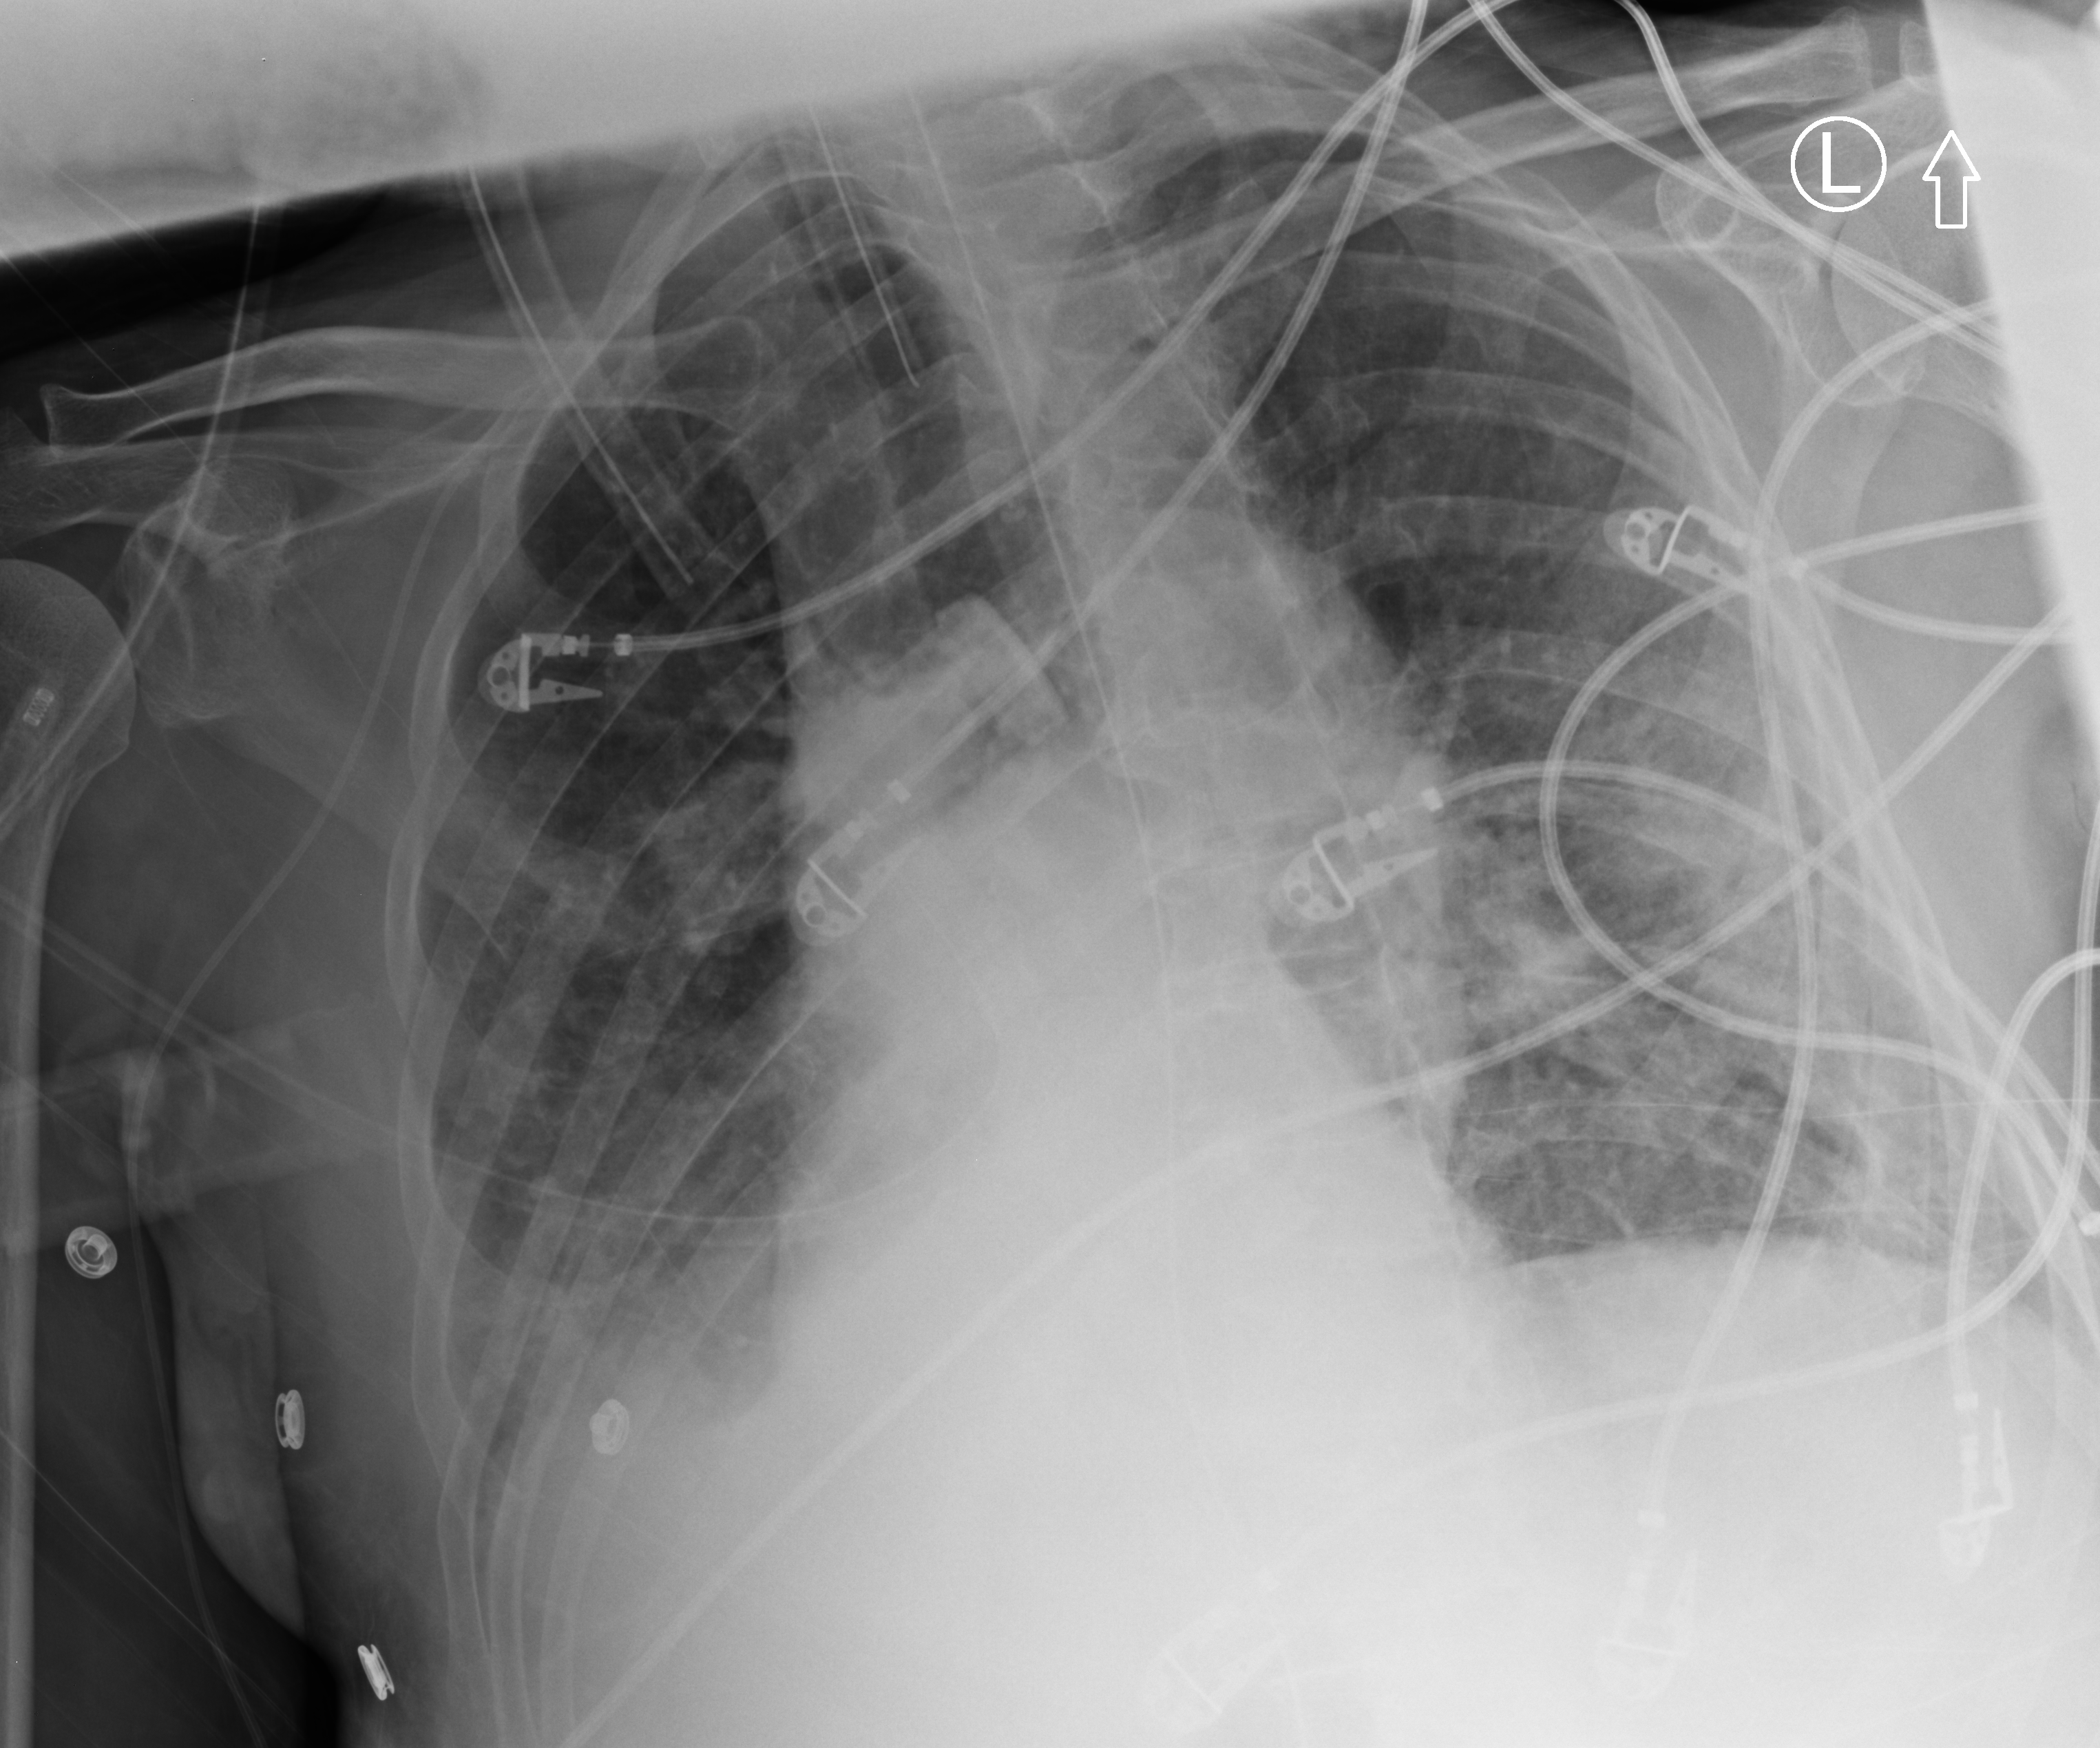
Bedside chest radiograph (computed radiography); anteroposterior (AP) projection. Patient hospitalised with COVID-19; male, aged 75–90 years.
Admission-level facts for this patient (not findings on this image; timing relative to this image not recorded): admitted to intensive care during this hospital stay: yes; smoking status (admission record): never; mechanically ventilated during this hospital stay: yes.